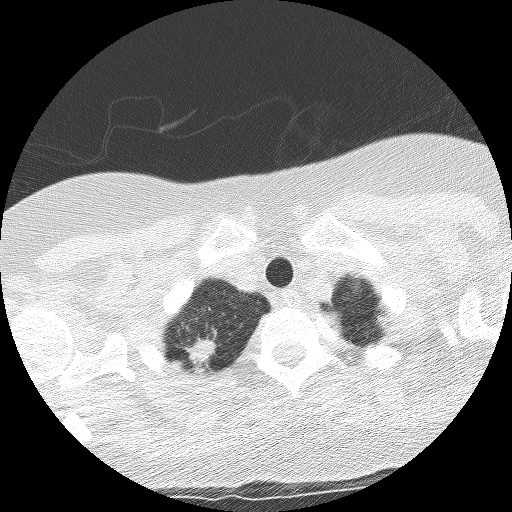
Low-dose screening chest CT, axial slice. Third annual screen. Lung window (W 1500 / L -600 HU). Lung (sharp) reconstruction kernel (BONE). Slice 11 of 130 in the series. 512 × 512 image matrix. Female participant, aged 56 years at enrolment.
Lesion marked by an expert reader, bounding box <169,328,224,376> (left, top, right, bottom; pixels). Screening reader's record for this exam (one nodule recorded; not confirmed to be the boxed lesion): non-calcified nodule or mass ≥4 mm, right upper lobe, 17 × 10 mm, spiculated (stellate) margins, mixed attenuation, pre-existing on the prior screen: yes; interval growth: yes. Official screen result: positive, other. Lung cancer was diagnosed 24 days after this screen: large cell carcinoma, NOS, right upper lobe, poorly differentiated (G3), stage IB (AJCC 6th edition), 15 mm at pathology.